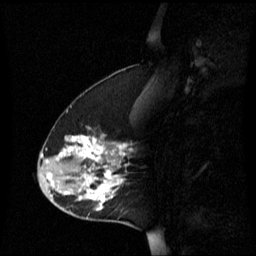
Breast MRI (dynamic contrast-enhanced), one sagittal slice; slice 23 of 60 in the series (ordered by position); dynamic contrast-enhanced series, image 2 of 3 at this slice position (ordered by acquisition); 1.5 T; TE 4.2 ms, TR 8.4 ms; 2.2 mm slice thickness; 256 × 256 image matrix, field of view 240 × 240 mm. Female patient, age 45 years. Case-level facts recorded for this patient, not image findings: setting: breast cancer imaged before/during neoadjuvant chemotherapy; receptor status: HR-positive, HER2-negative.
Outlined on this slice (semi-automatic segmentation, software-assisted and operator-edited):
- analysis volume of interest (the breast-tissue region the enhancement analysis was run in; not a lesion): bounding box (x1, y1, x2, y2) in pixels: (38, 128, 133, 221)
- tumour enhancement mask (voxels above the 70 % enhancement threshold inside the analysis volume of interest): (46, 134, 125, 209)